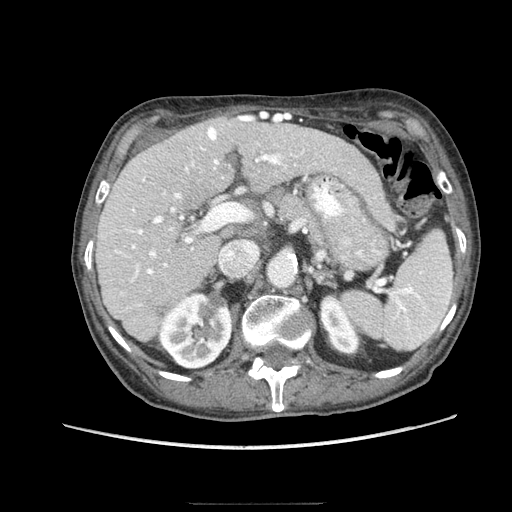
Contrast-enhanced abdominal CT (liver protocol), one axial slice. Slice 48 of 83 in the series (ordered by position). 140 kVp. Soft-tissue window (W 400 / L 40 HU). 2.5 mm slice thickness. 512 × 512 image matrix, field of view 360 × 360 mm. Case-level facts recorded for this patient, not image findings: diagnosis: hepatocellular carcinoma (patient treated with transarterial chemoembolisation; whether this scan precedes or follows treatment is not stated here); TNM stage (as recorded): Stage-I; Child-Pugh class: A; tumour nodularity: uninodular.
Structures marked on this image (semi-automatic segmentation, software-assisted and operator-edited):
- liver parenchyma outside the tumour (the mass and vessels are separate outlines, so this box may not span the whole liver): bounding box (x1, y1, x2, y2) in pixels: (96, 114, 362, 342)
- liver vessels: (115, 116, 315, 306)